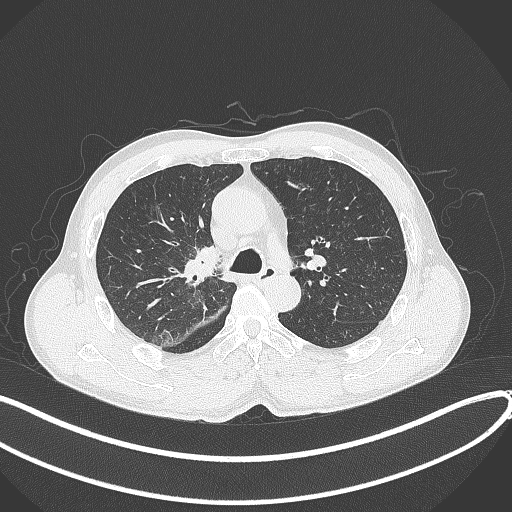
Chest CT, one axial slice. Position 261 of 409 along the scan axis. Reconstruction kernel B70f. 120 kVp. Lung window (W 1500 / L -600 HU). 1 mm slice thickness. 512 × 512 image matrix, field of view 400 × 400 mm. Male patient, age 53 years. From the clinical record (not read from this slice): clinical TNM (as recorded): T1b N0 M0.
Annotated regions visible in this slice (bounding box drawn by a radiologist):
- lung tumour (recorded histology: squamous cell carcinoma): bounding box <179,243,221,290> (left, top, right, bottom; pixels)